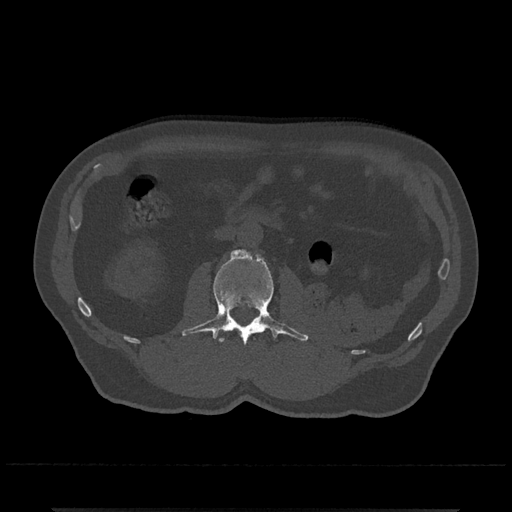
CT including the spine, one axial slice; slice 293 of 797 in the series (ordered by position); reconstruction kernel Br40s/3; 120 kVp; bone window (W 1800 / L 400 HU); 0.5 mm slice thickness; 512 × 512 image matrix. Patient: male, 67 years. Case-level facts recorded for this patient, not image findings: primary cancer: prostate.
Outlined on this slice (semi-automatic segmentation, software-assisted and operator-edited):
- L2 vertebra: bounding box [x1, y1, x2, y2] px = [181, 249, 309, 345]